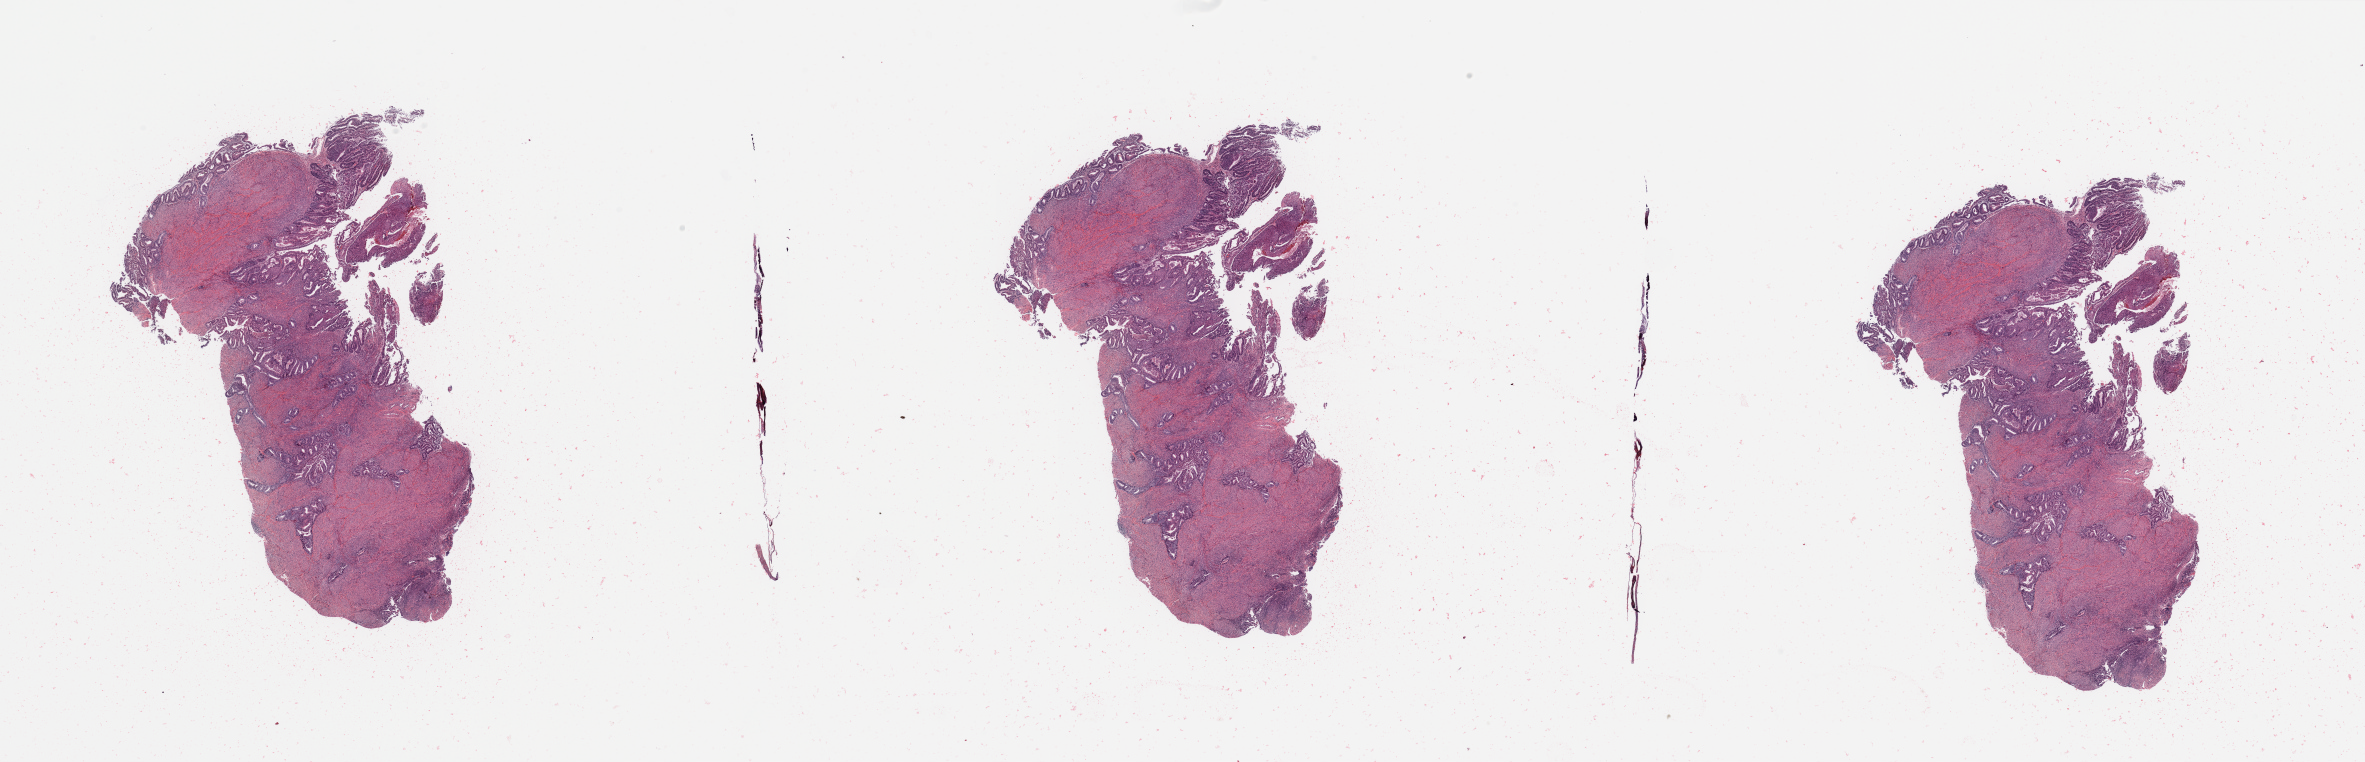
H&E whole-slide image — shown as a low-resolution overview of the whole scanned area (about 37.4 x 12.1 mm). Uterus, tumour tissue. Patient: female, age 62 years.
Diagnosis: Endometrioid adenocarcinoma, NOS.